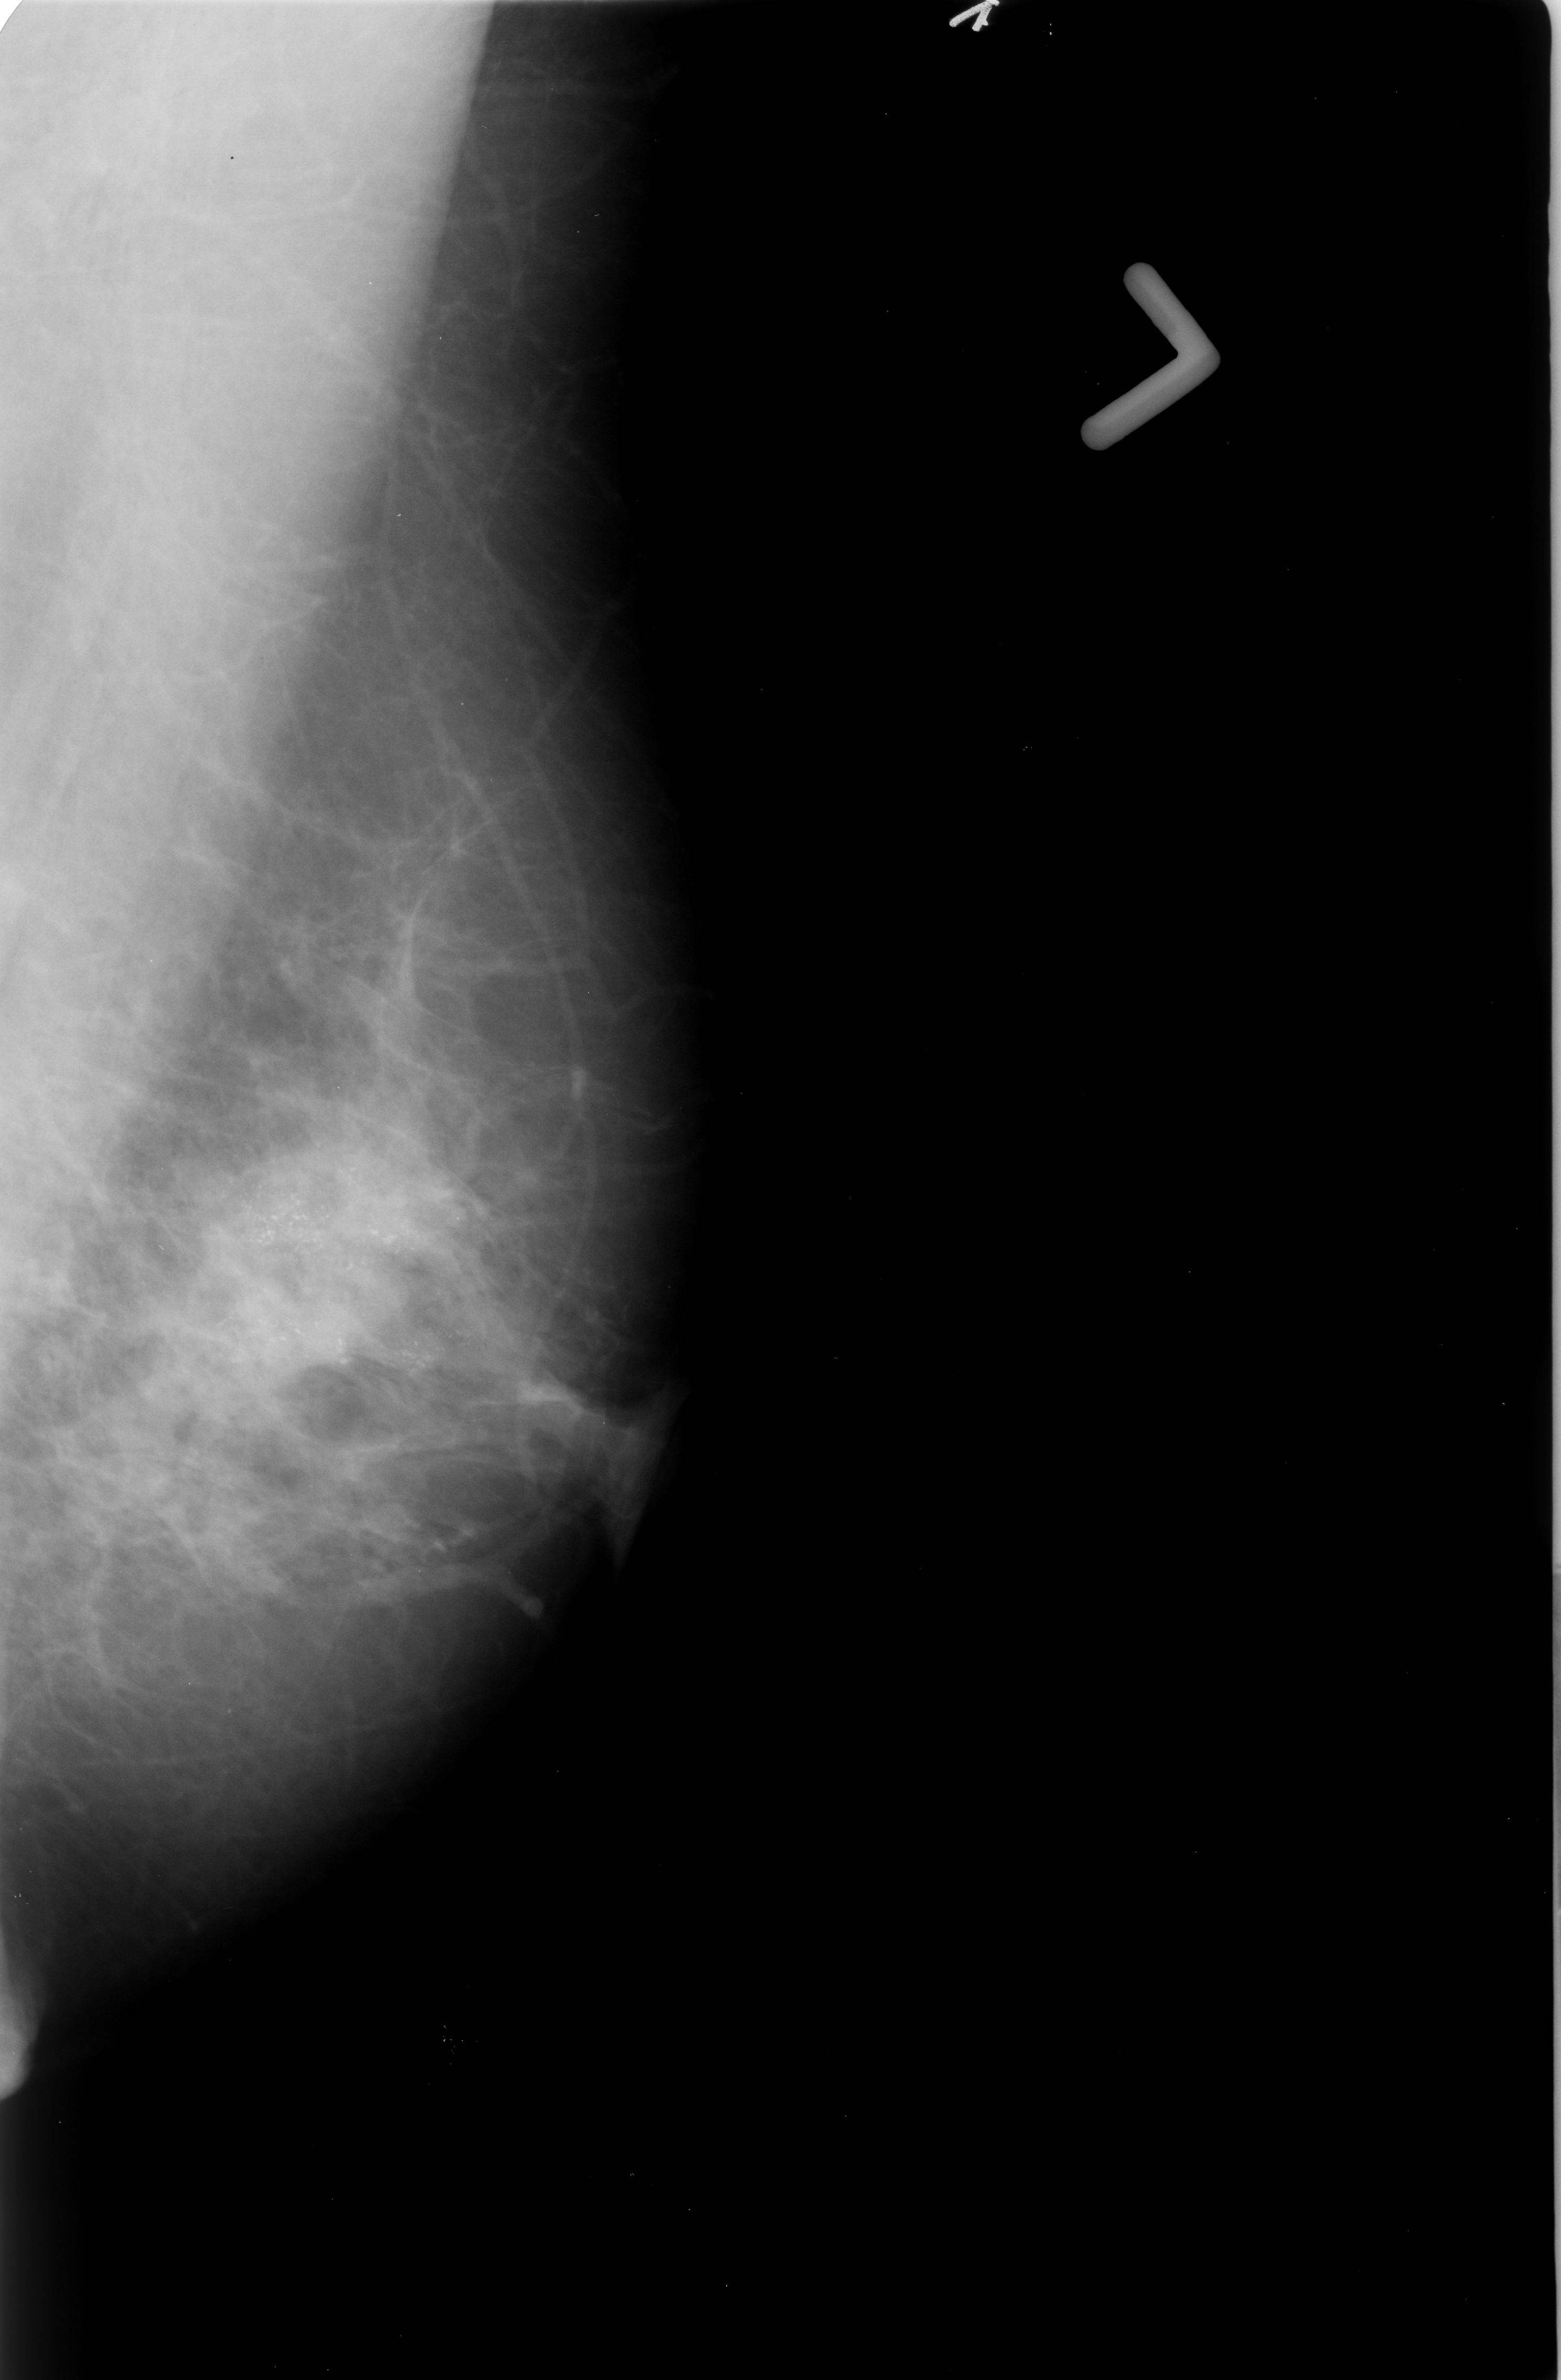
Digitized screen-film mammogram, left breast, MLO view, BI-RADS breast density category 2 (scale 1–4).
- Marked findings (only marked abnormalities are described; nothing is implied about the rest of the image): calcifications, morphology pleomorphic, distribution segmental; BI-RADS assessment category 5; subtlety rating 5 on a 1 (subtle) to 5 (obvious) scale; pathology result (as recorded, not read from the image): malignant.